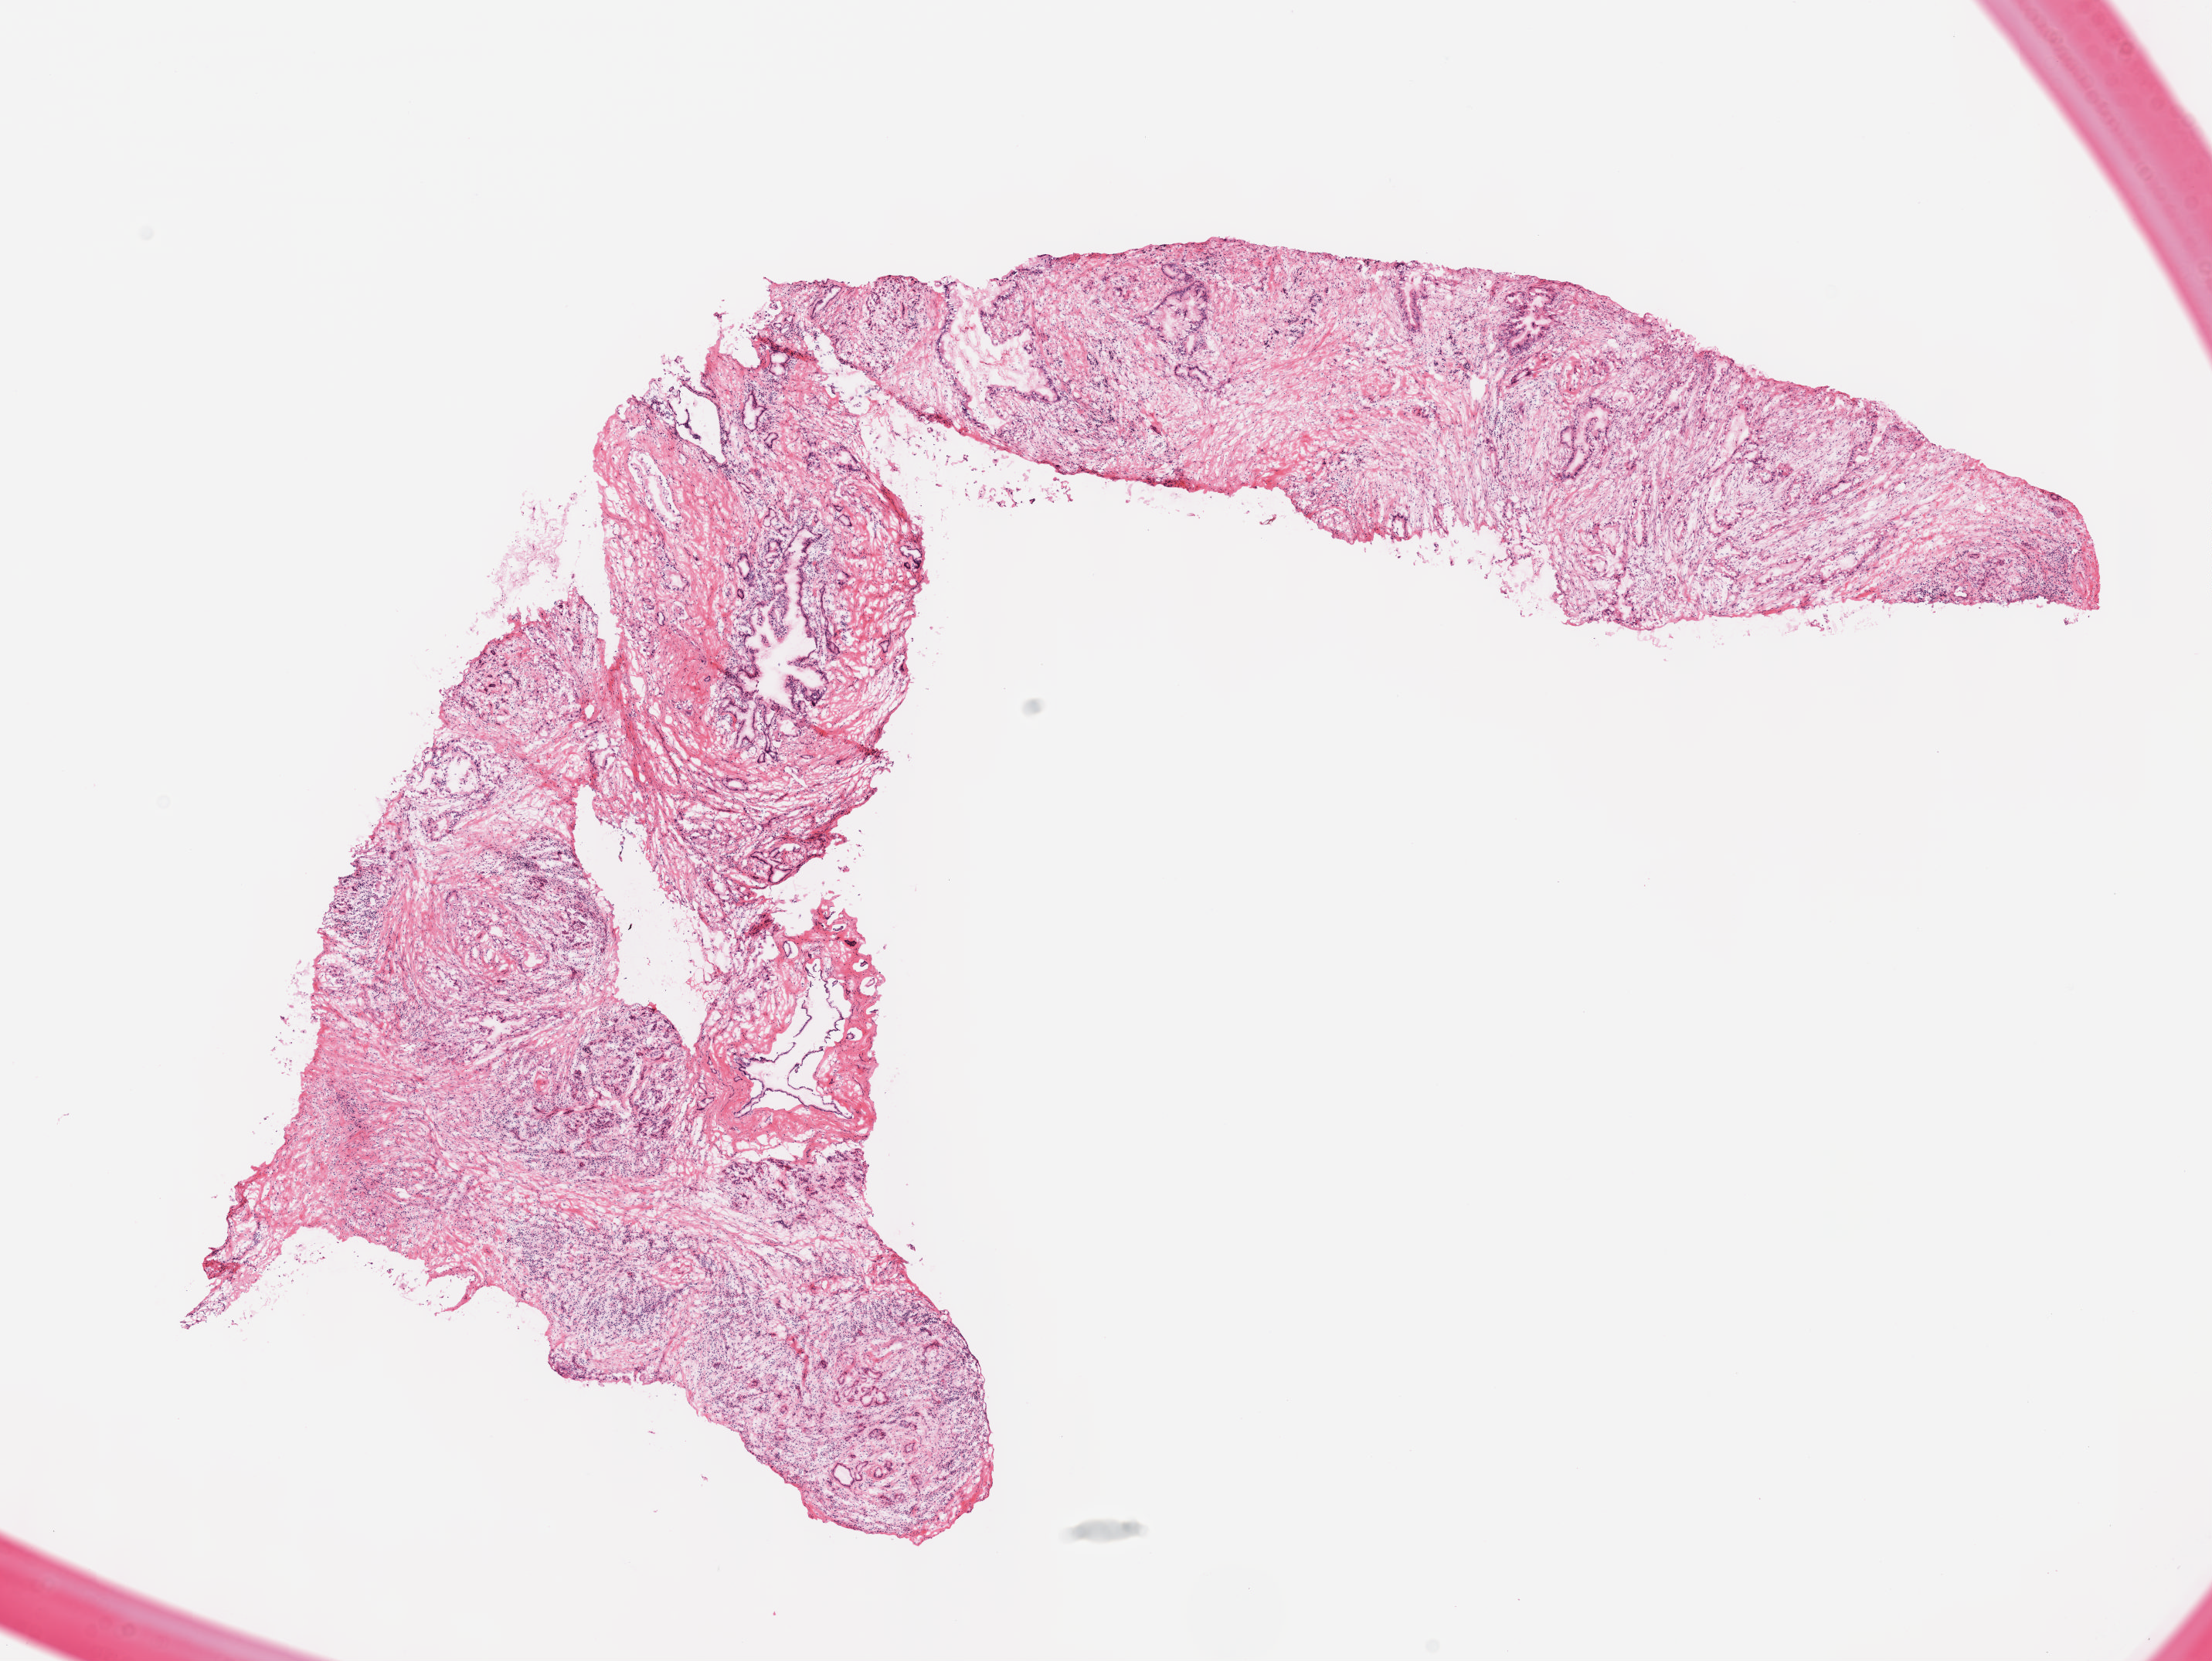
Whole-slide histology image, Hematoxylin and eosin (H&E) stained — low-resolution overview of the scanned area, about 11.6 x 8.7 mm (slide scanned at 40x); formalin-fixed paraffin-embedded (FFPE) diagnostic section; primary tumour sample from the pancreas. Male, age 71 years at initial diagnosis. Histologic grade: G2 (moderately differentiated).
AJCC pathologic stage: IIB (7th edition). TNM: T2 N1 MX. Pathologic diagnosis: Infiltrating duct carcinoma, NOS (head of pancreas).